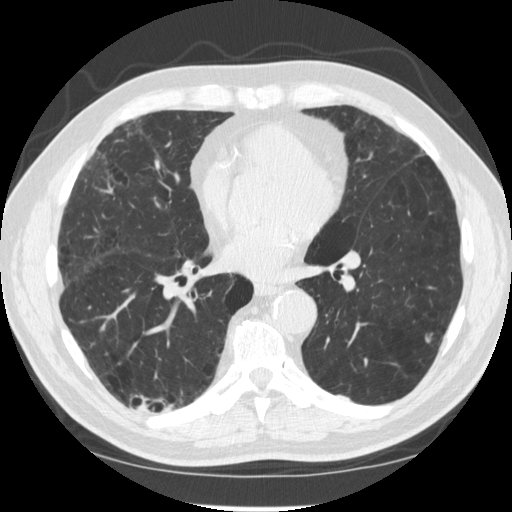
Low-dose screening chest CT, axial slice. Second screening round (one year after baseline). Lung window (W 1500 / L -600 HU). 1.25 mm slice thickness. Standard (soft-tissue) reconstruction kernel (STANDARD). Male, age 70 years at enrolment.
Expert reader's lesion annotation, bounding box [x1, y1, x2, y2] px = [124, 376, 175, 432]. The screening reader recorded 2 non-calcified nodules or masses ≥4 mm on this exam (right lower lobe, right lower lobe); which of them this box marks is not recorded. Lung cancer was diagnosed 617 days after this screen: squamous cell carcinoma, NOS, right upper lobe, poorly differentiated (G3), stage IV (AJCC 6th edition).